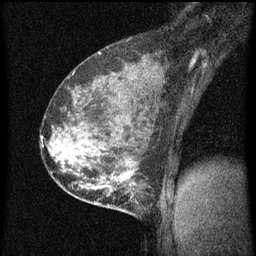
Breast MRI (dynamic contrast-enhanced), one sagittal slice. Slice 38 of 60 in the series (ordered by position). Dynamic contrast-enhanced series, image 2 of 3 at this slice position (ordered by acquisition). 1.5 T. TE 4.2 ms, TR 8 ms. 2 mm slice thickness. 256 × 256 image matrix. Female patient, age 35 years.
Outlined on this slice (semi-automatically segmented with operator editing):
- analysis volume of interest (the breast-tissue region the enhancement analysis was run in; not a lesion): bounding box [x1, y1, x2, y2] px = [110, 178, 155, 219]
- tumour enhancement mask (voxels above the 70 % enhancement threshold inside the analysis volume of interest): [110, 178, 139, 205]